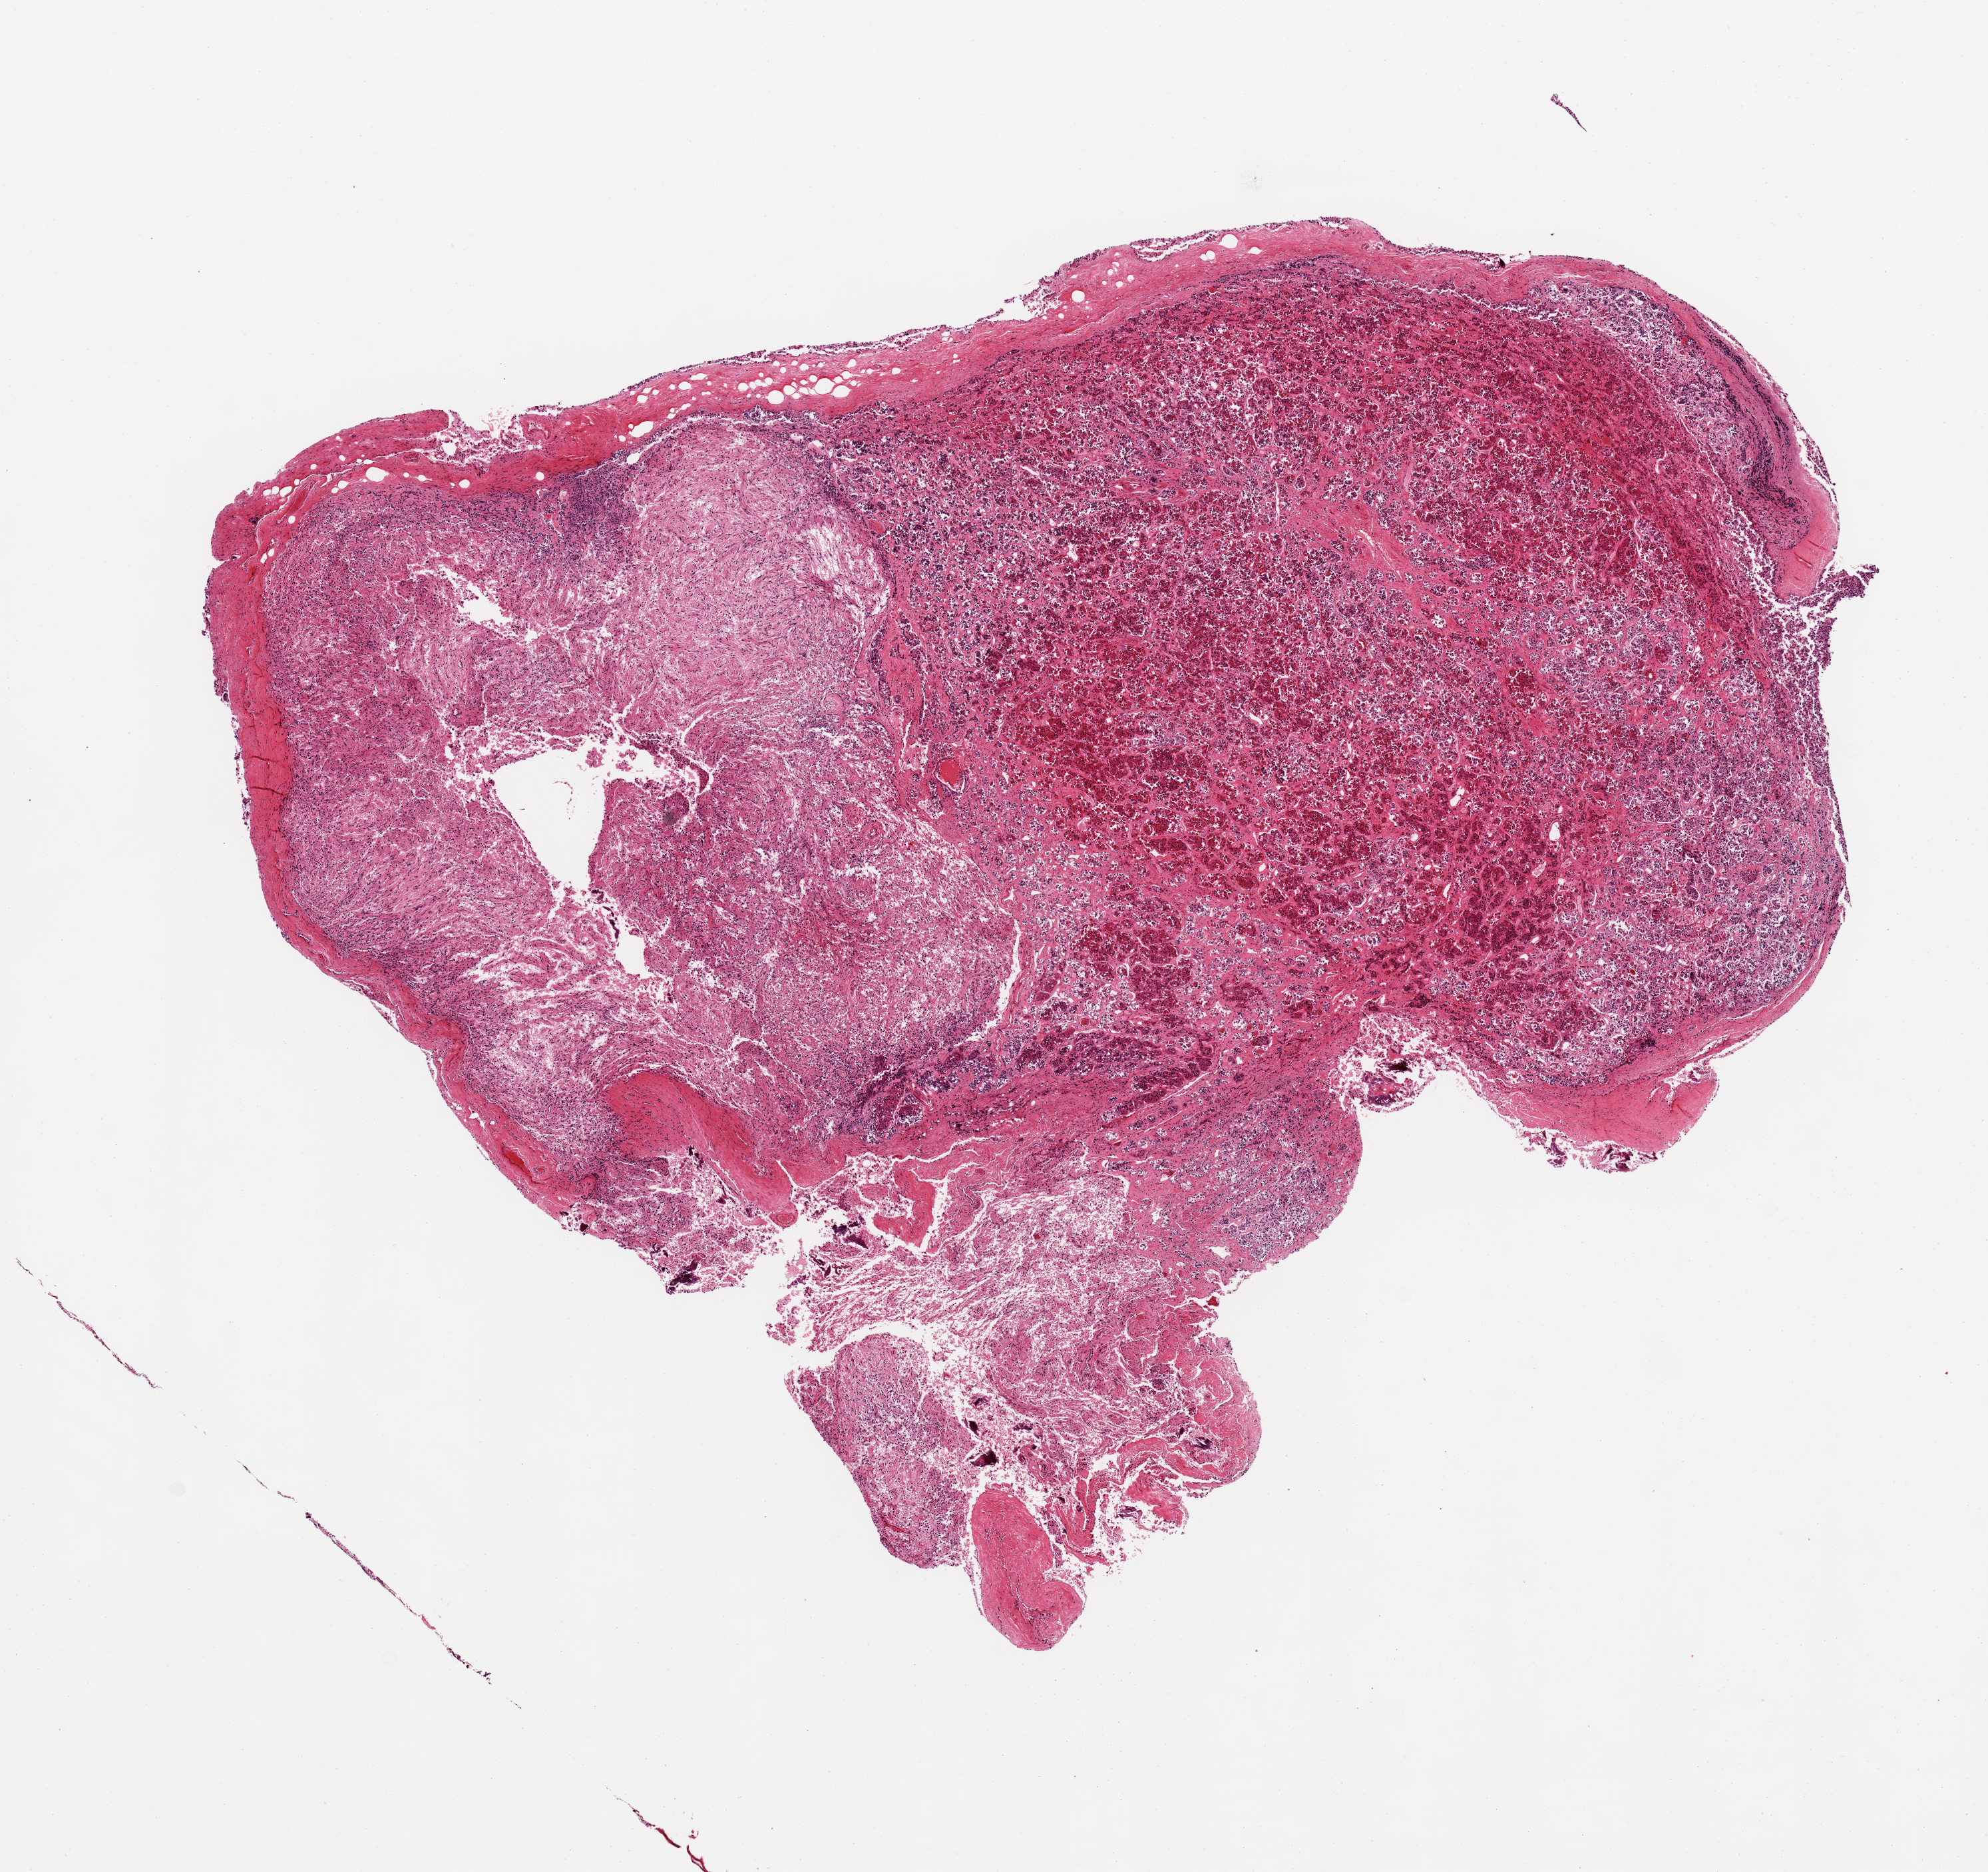
Digitized haematoxylin and eosin-stained section, brightfield — a low-resolution overview of the entire scanned area, about 11.8 x 11.1 mm (acquisition: 20x scan). PAXgene-fixed paraffin-embedded (PFPE) section. Section of pituitary (target tissue). Tissue donor sample. Male donor.
Review note (as recorded): 1 piece, 9.6x7.3 mm; about half anterior, half posterior pituitary.